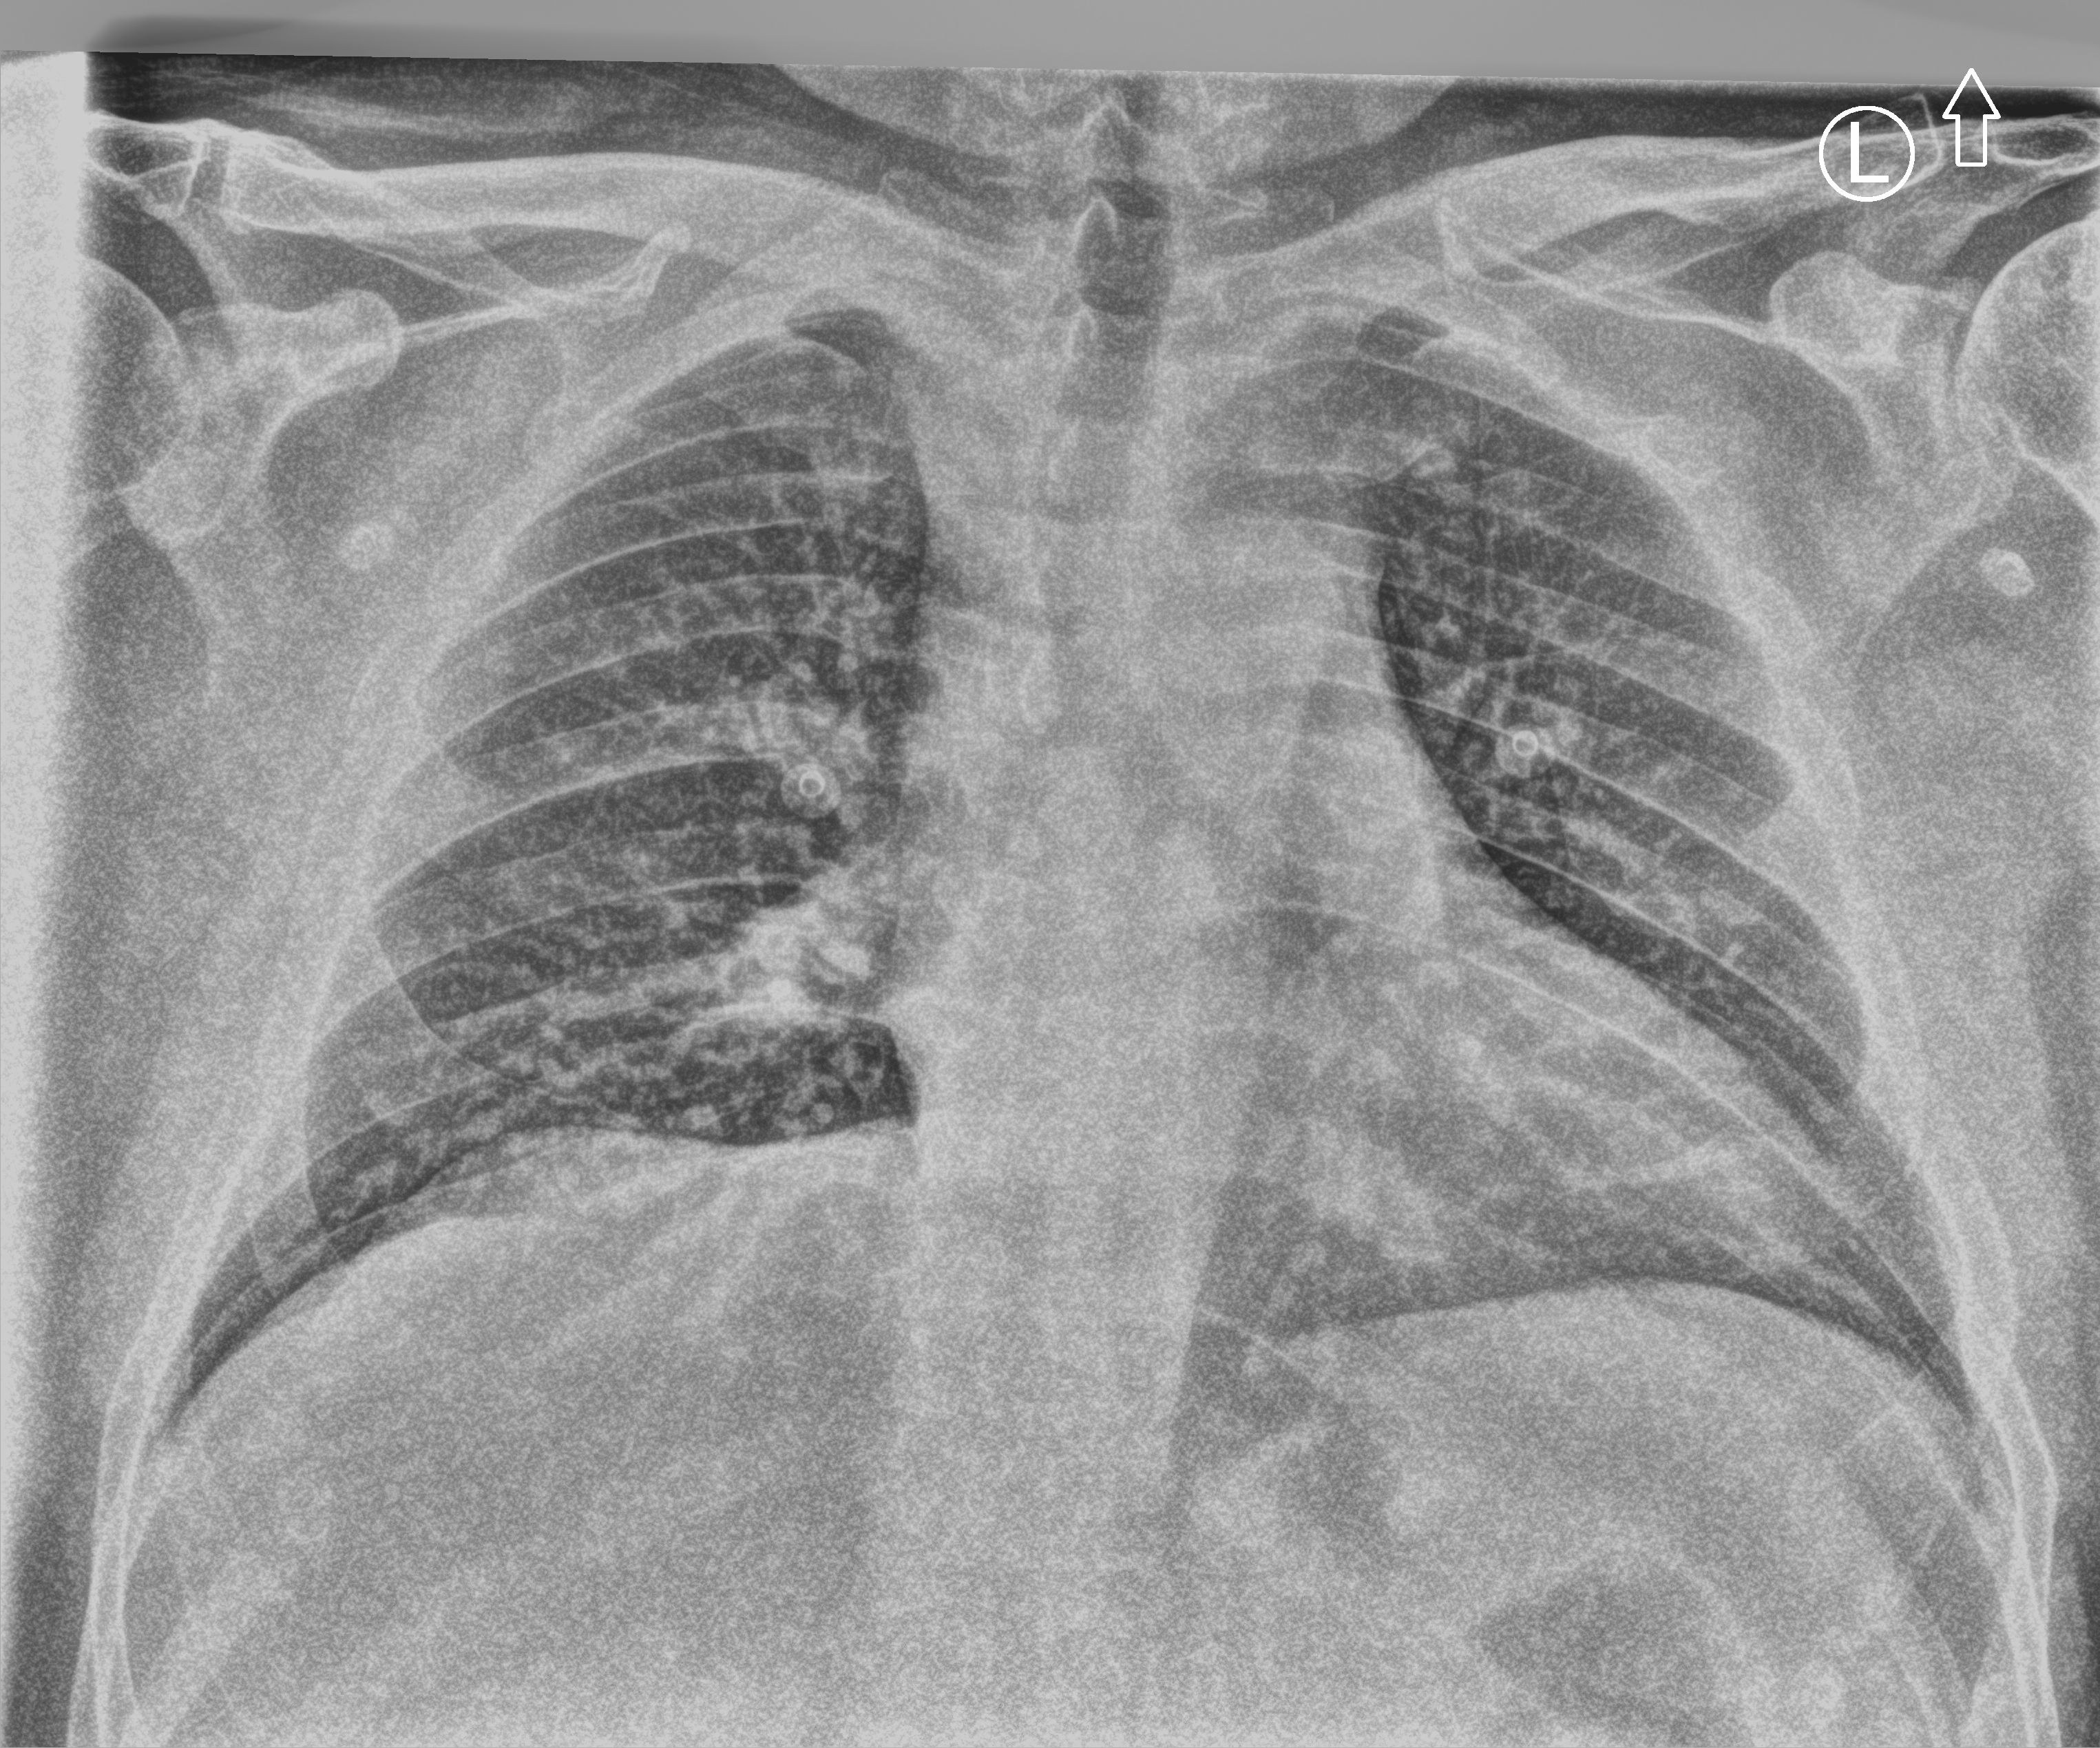
Portable chest radiograph; anteroposterior (AP) projection. Male patient hospitalised with COVID-19, age 18–59 years.
Hospital-stay facts (about this admission, not read from this image; timing relative to this image not recorded):
- admitted to intensive care during this hospital stay: no